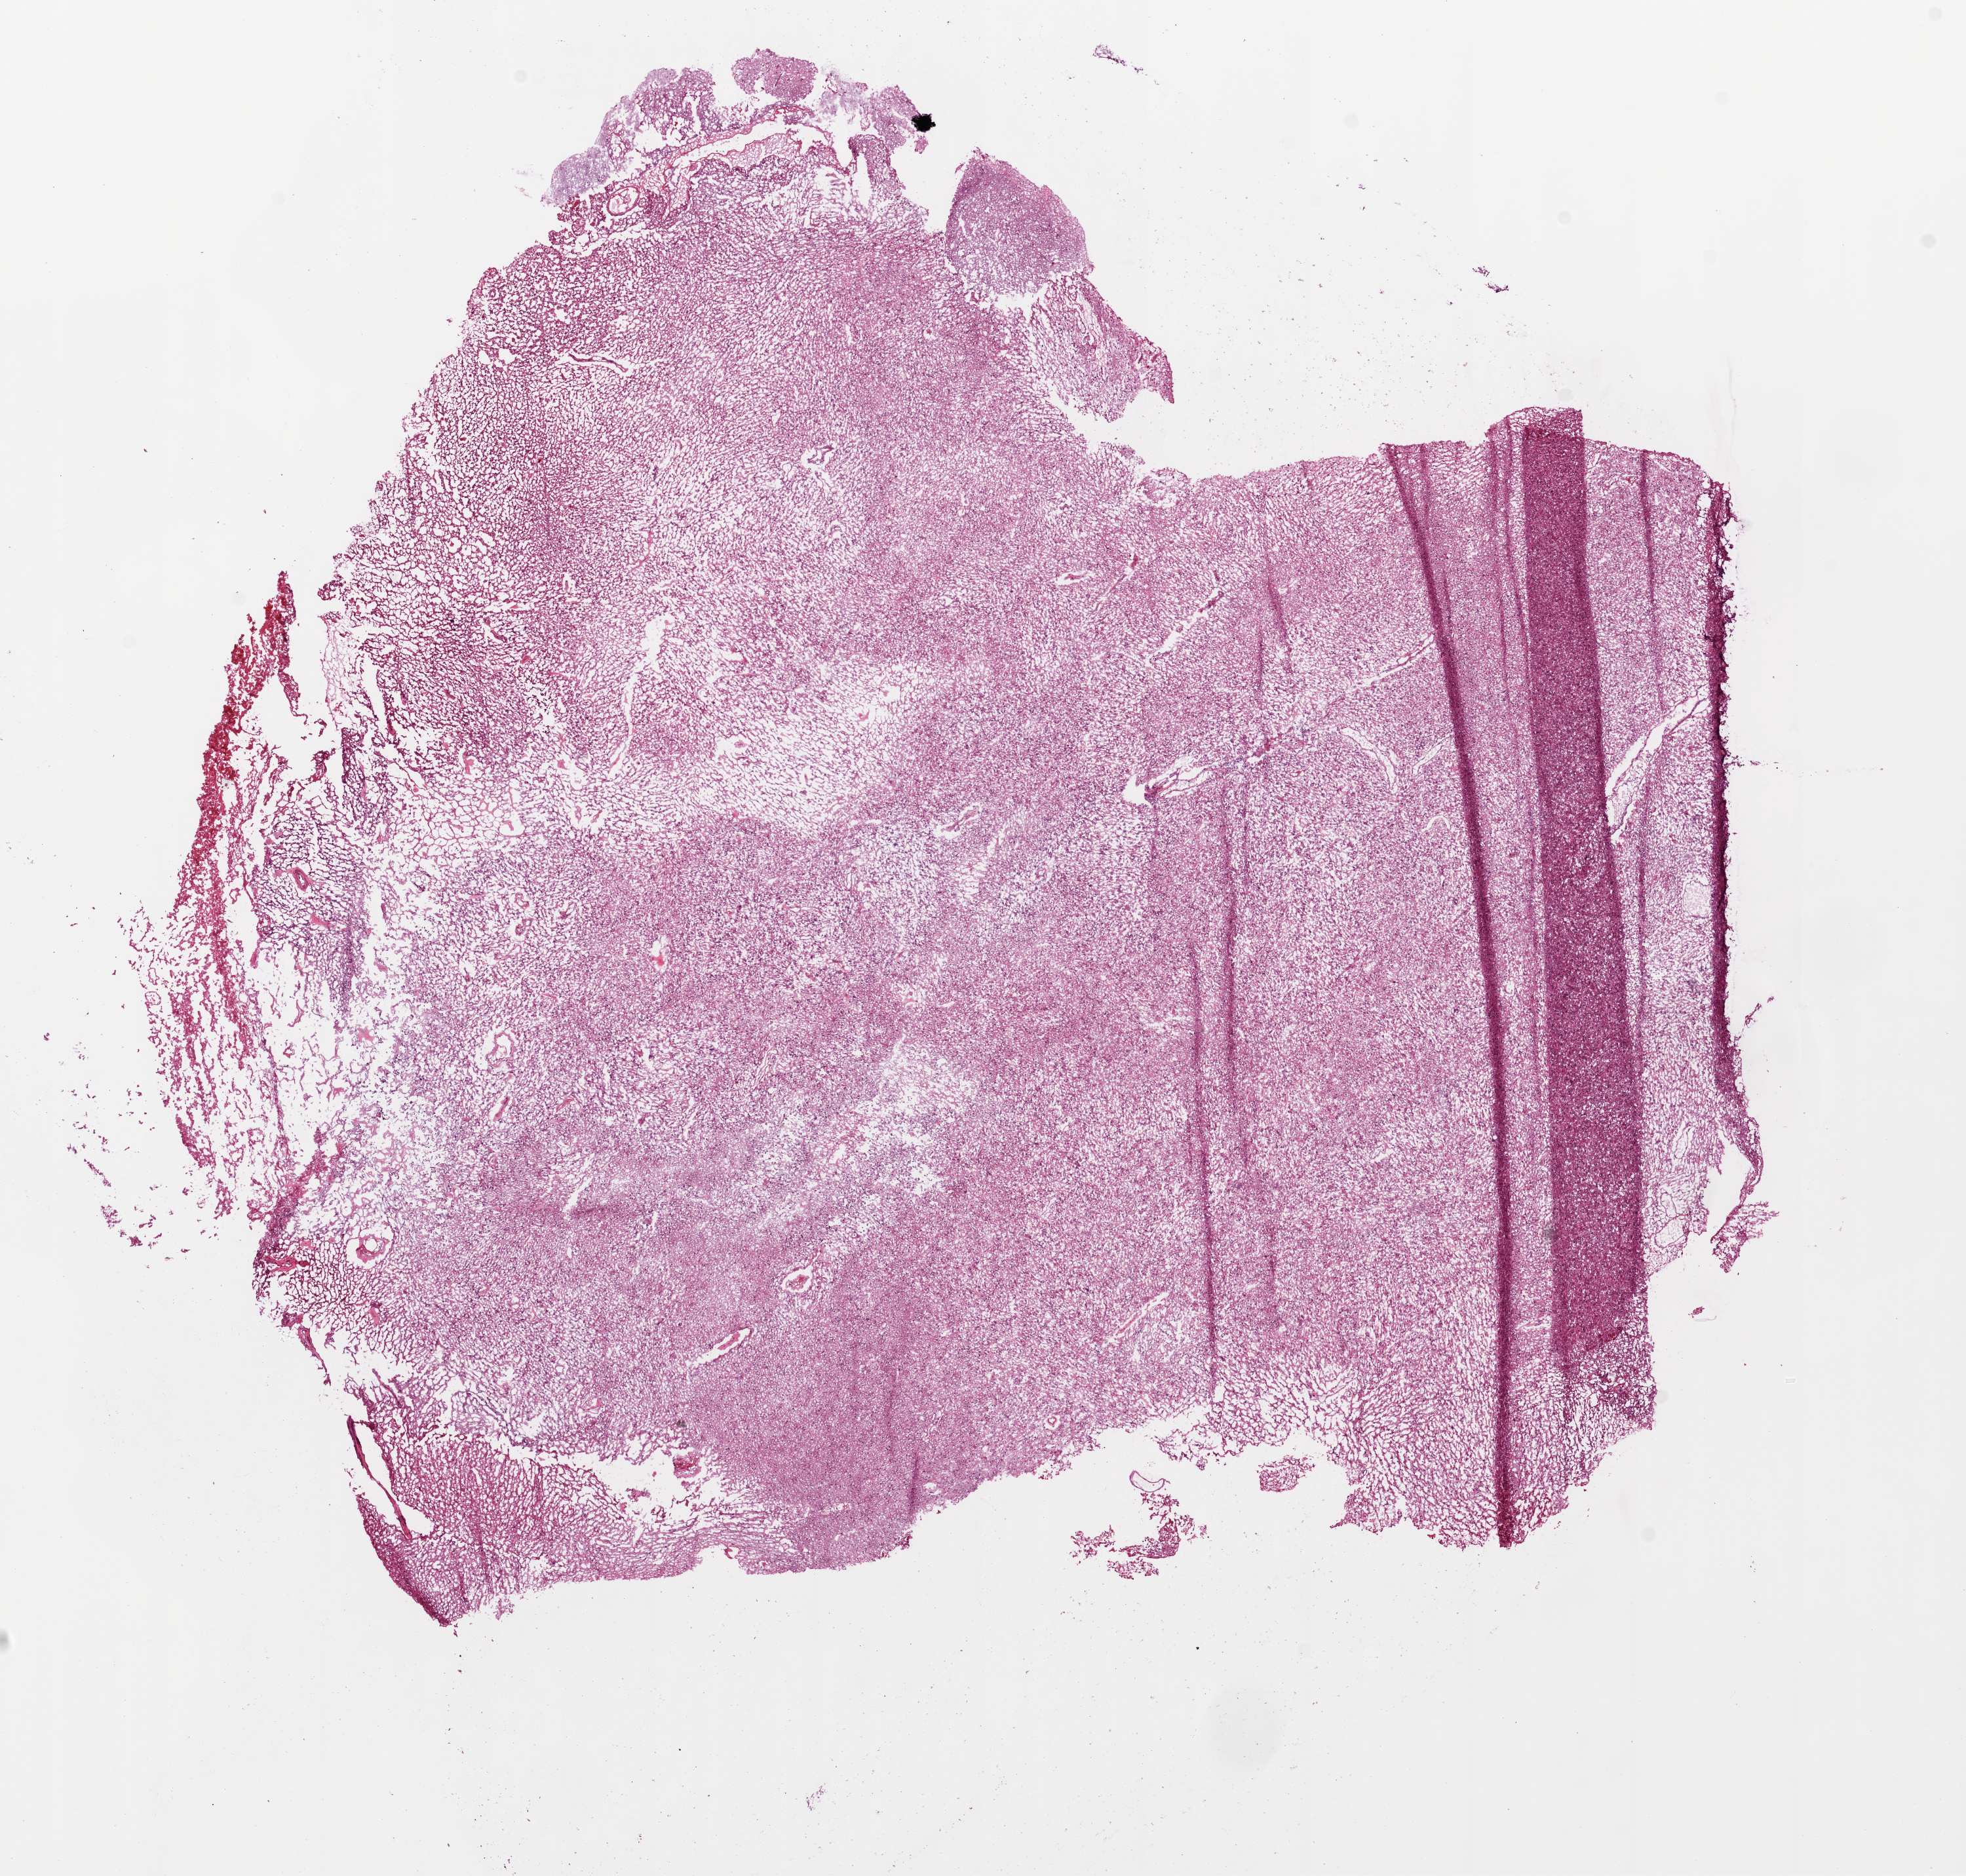
Whole-slide histology image, H&E-stained — shown as a low-resolution overview of the whole scanned area (about 12.0 x 11.5 mm, from a 20x scan), frozen section from the top of the tissue portion, primary tumour sample from the brain. Patient: male, age at initial diagnosis 64 years. Slide review estimates, as recorded: tumour cells 100%, tumour nuclei 80%, normal cells 0%, stromal cells 0%, necrosis 0%.
• histologic diagnosis: Glioblastoma